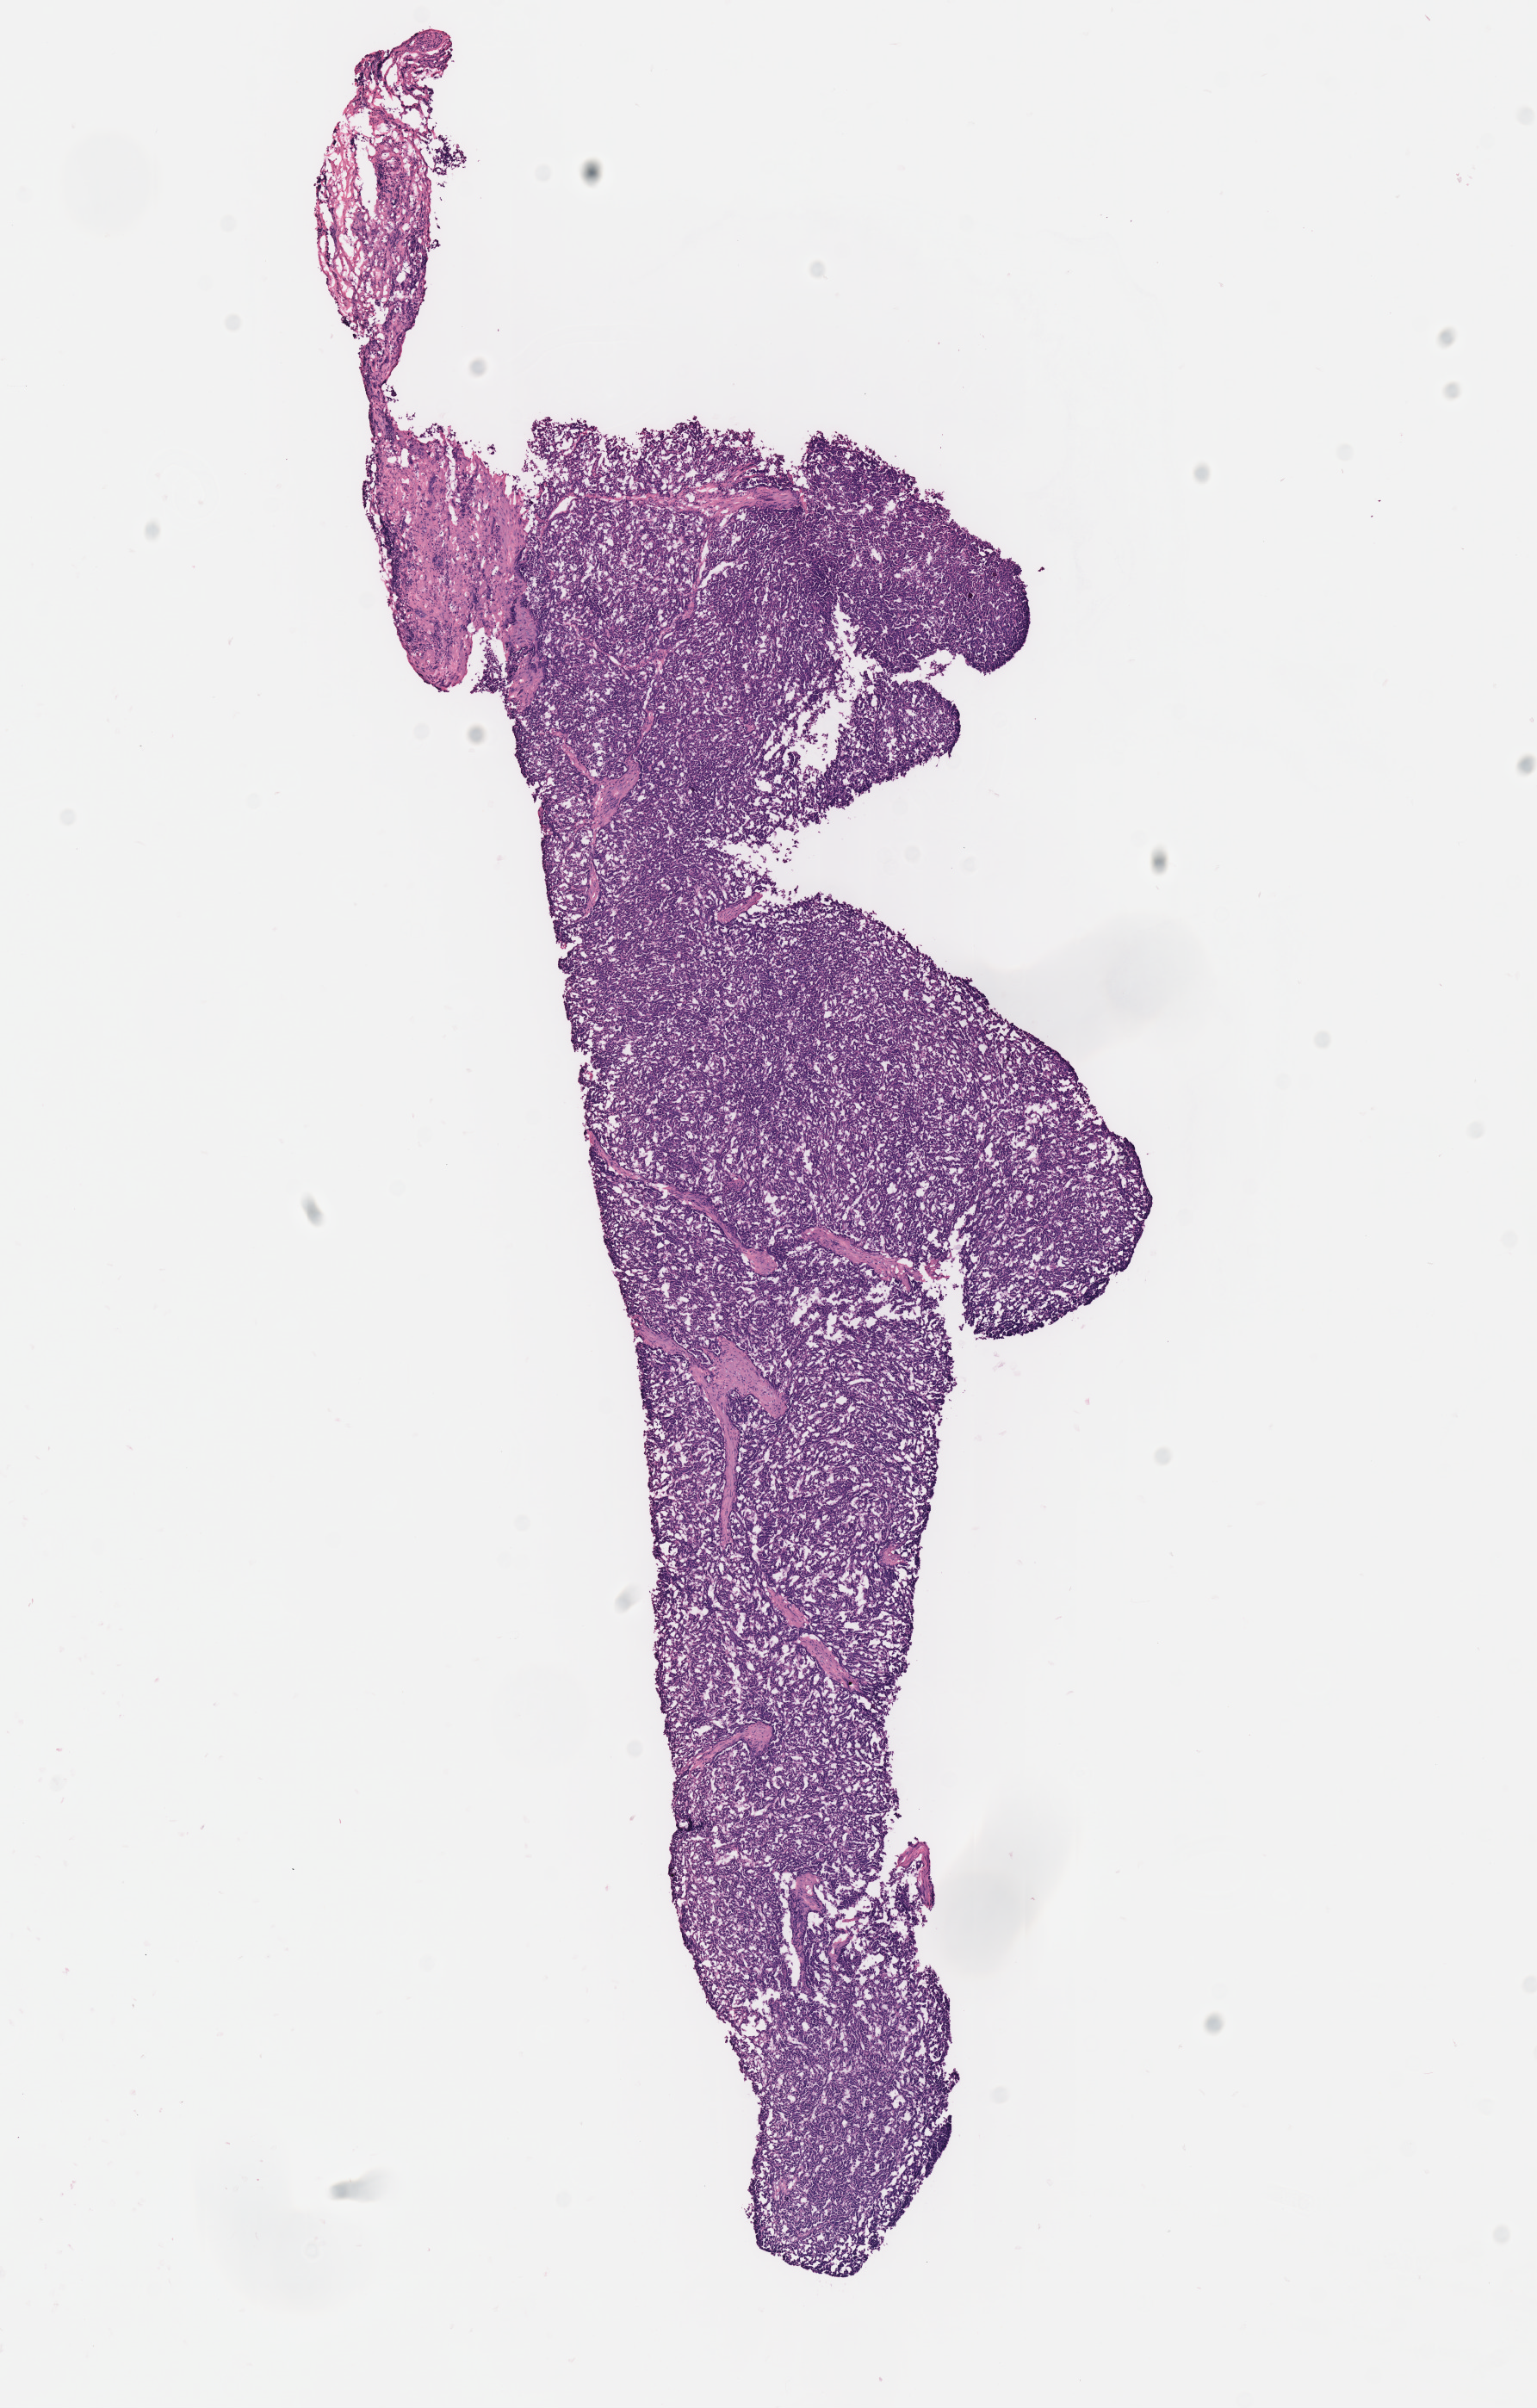
H&E whole-slide image — a low-resolution overview of the entire scanned area, about 7.0 x 11.0 mm. Frozen section from the top of the tissue portion. Primary tumour sample from the kidney. Male patient; age at initial diagnosis 55 years. Slide review estimates, as recorded: tumour cells 100%, tumour nuclei 90%, normal cells 0%, stromal cells 0%, necrosis 0%. Infiltration values recorded for this section: lymphocyte infiltration 0%, monocyte infiltration 0%, neutrophil infiltration 0%.
- TNM: T1a NX MX
- diagnosis: Papillary adenocarcinoma, NOS
- AJCC pathologic stage: I (6th edition)